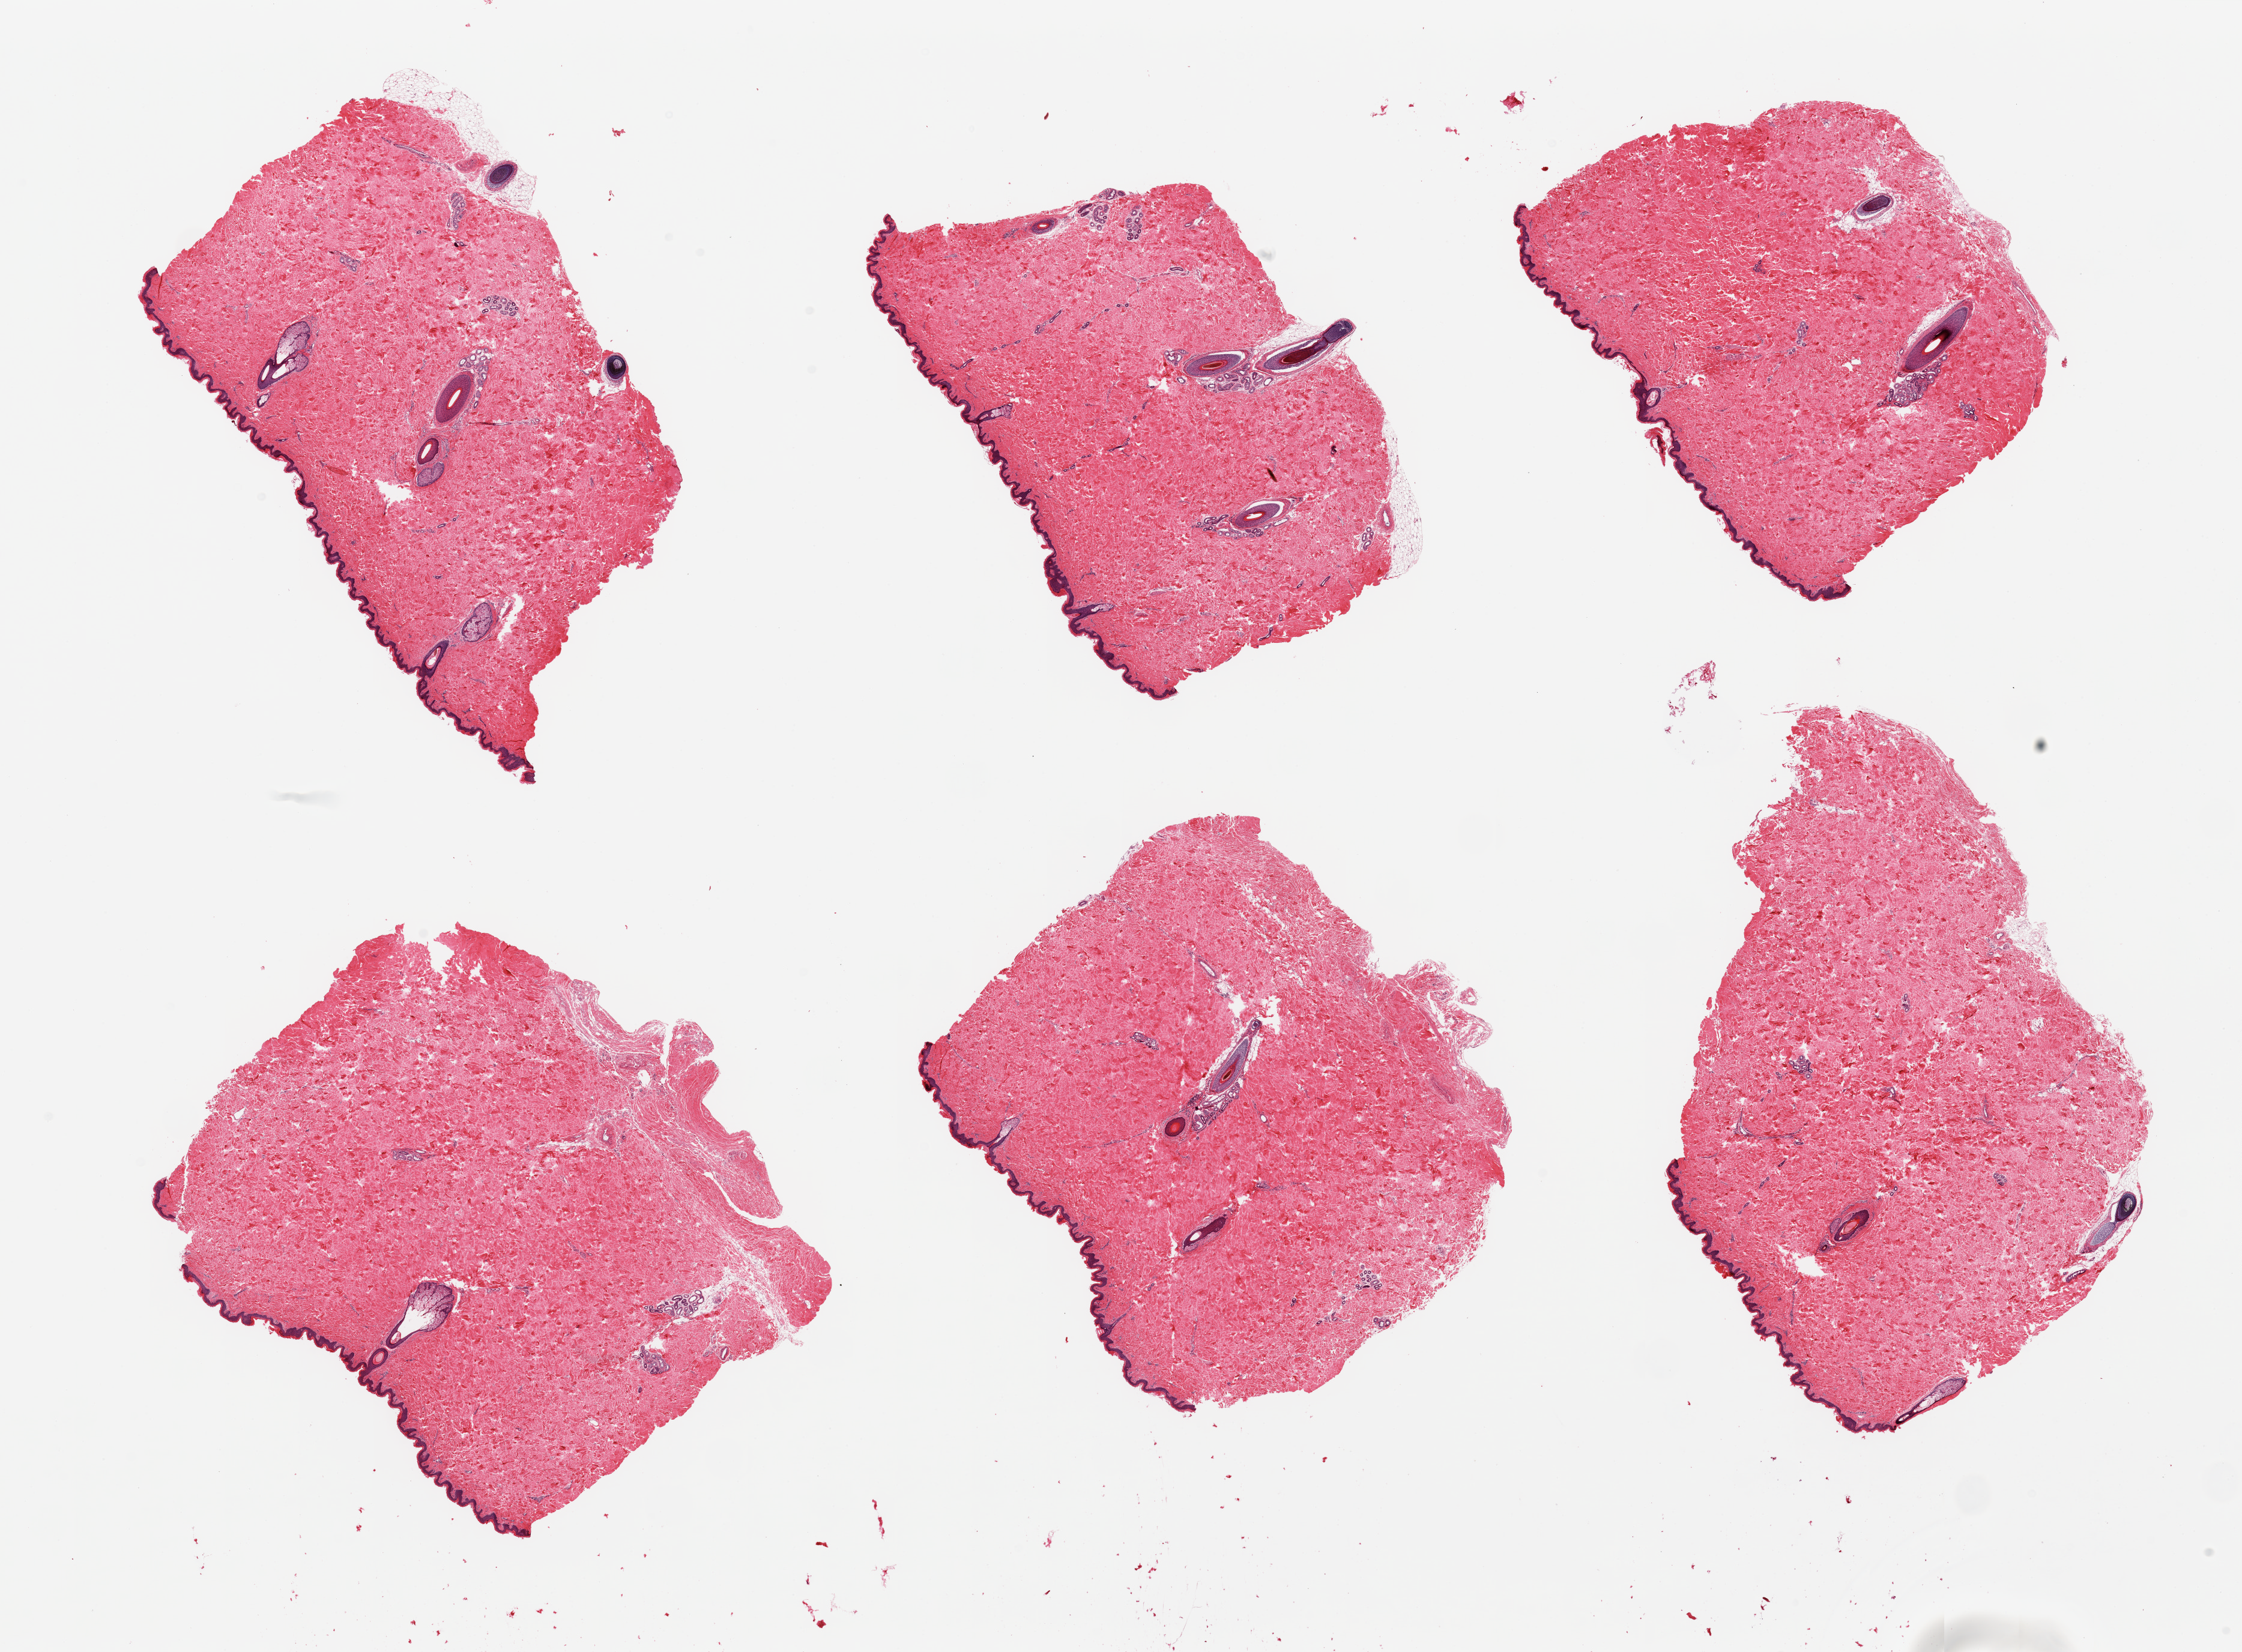
Haematoxylin and eosin whole-slide image, shown as a low-resolution overview of the whole scanned area (about 29.5 x 21.8 mm). PAXgene-fixed, paraffin-embedded tissue. Target tissue: skin of suprapubic region. Tissue donor sample. Donor sex: male.
Pathologist's review note for this sample: 6 pieces; up to 3 hair follicles in each piece; well trimmed; <1% intradermal fat.